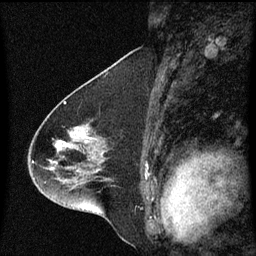
Breast MRI (dynamic contrast-enhanced), one sagittal slice. Slice 36 of 60 in the series (ordered by position). Dynamic contrast-enhanced series, image 2 of 3 at this slice position (ordered by acquisition). 1.5 T. TE 4.2 ms, TR 8.4 ms. 256 × 256 image matrix. Female patient, age 46 years. Case-level facts recorded for this patient, not image findings: setting: breast cancer imaged before/during neoadjuvant chemotherapy; receptor status: HER2-positive.
Outlined on this slice (semi-automatically segmented with operator editing):
- analysis volume of interest (the breast-tissue region the enhancement analysis was run in; not a lesion): bounding box [x1, y1, x2, y2] px = [29, 112, 108, 195]
- tumour enhancement mask (voxels above the 70 % enhancement threshold inside the analysis volume of interest): [59, 142, 63, 143]